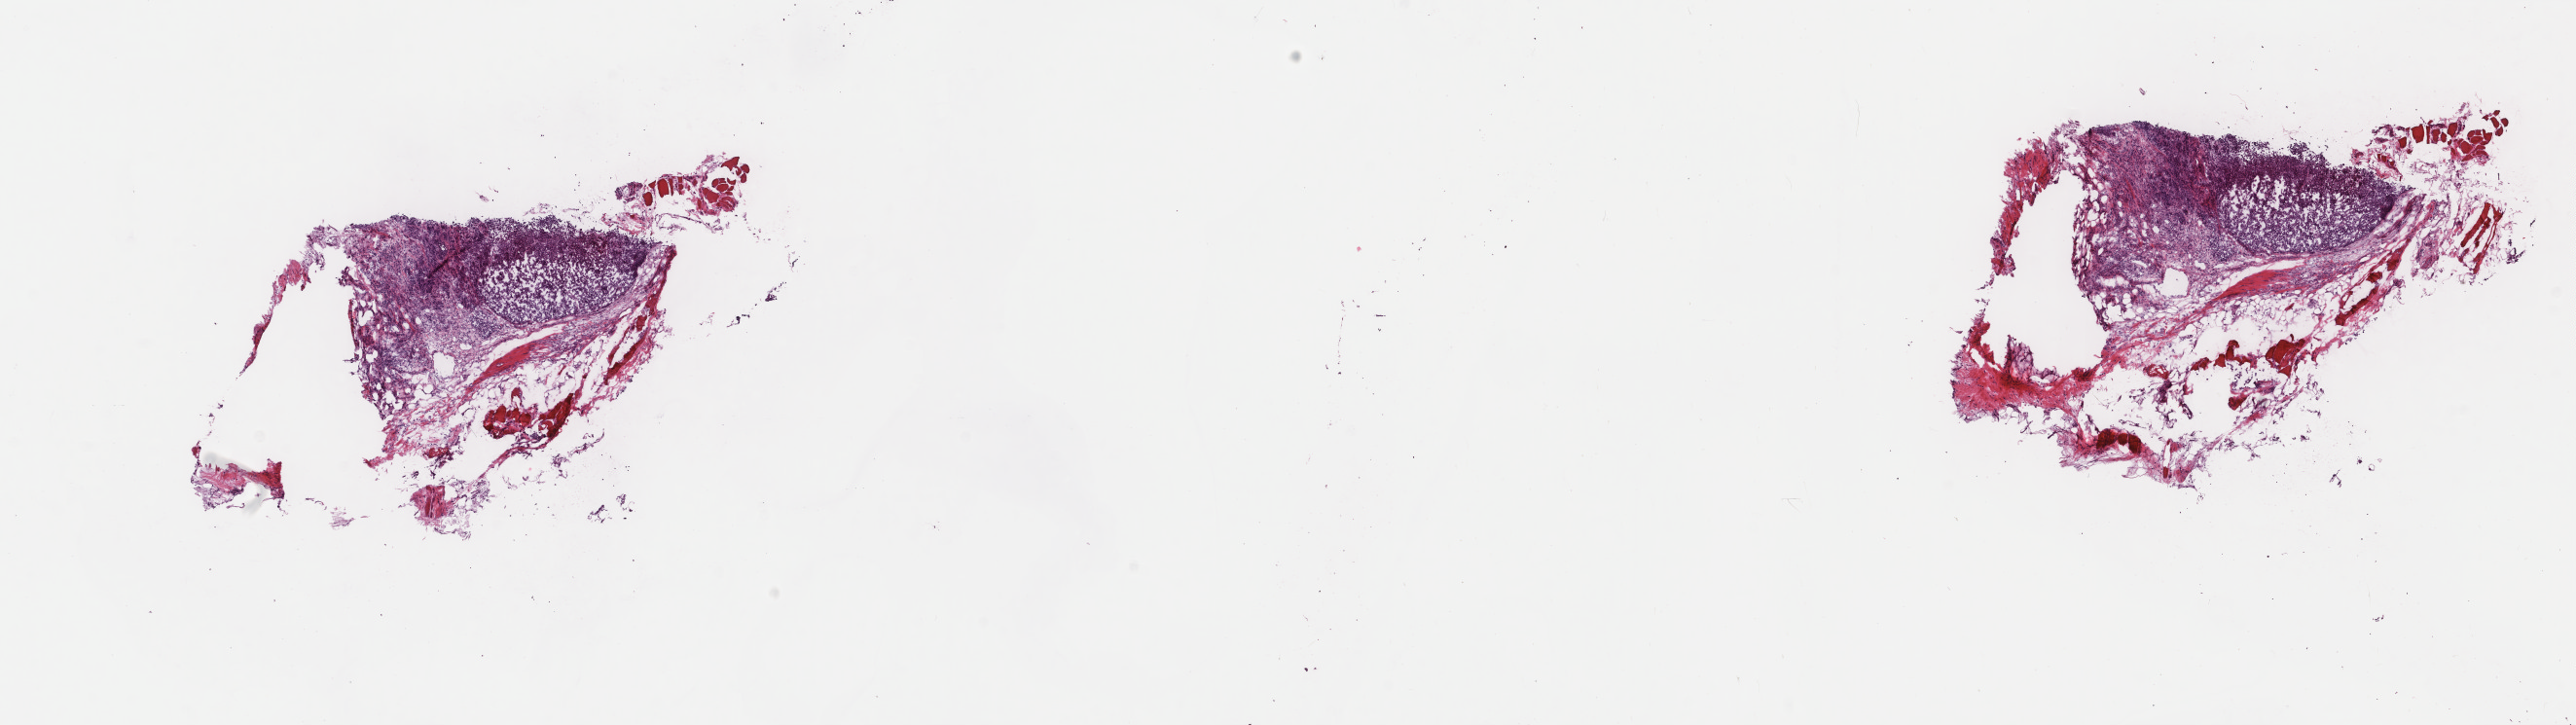
H&E-stained whole-slide image — low-resolution overview of the scanned area, about 21.0 x 5.9 mm (slide scanned at 40x). Frozen section. Metastatic tumour sample. Female patient; age at initial diagnosis 48 years. Composition of this section per pathologist review: tumour cells 70%, tumour nuclei 70%, normal cells 0%, stromal cells 30%, necrosis 0%. Infiltration values recorded for this section: lymphocyte infiltration 5%, monocyte infiltration 0%, neutrophil infiltration 0%.
This section: metastatic tumour tissue. Patient diagnosis: Malignant melanoma, NOS.